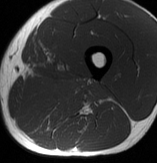
MRI of an extremity soft-tissue mass, one axial slice. Position 29 of 70 along the scan axis. MR volume resampled by the dataset authors to the PET/CT grid (not the native acquisition matrix). 3.27 mm slice thickness. 157 × 163 image matrix, field of view 153 × 159 mm. Male patient. Case-level facts recorded for this patient, not image findings: histological type: extraskeletal osteosarcoma; grade: high; site of the primary tumour: left adductur.
Annotated regions visible in this slice (expert contour drawn on MRI and transferred to this co-registered scan by the dataset authors):
- gross tumour volume (mass): bounding box (x1, y1, x2, y2) in pixels: (21, 71, 112, 130)